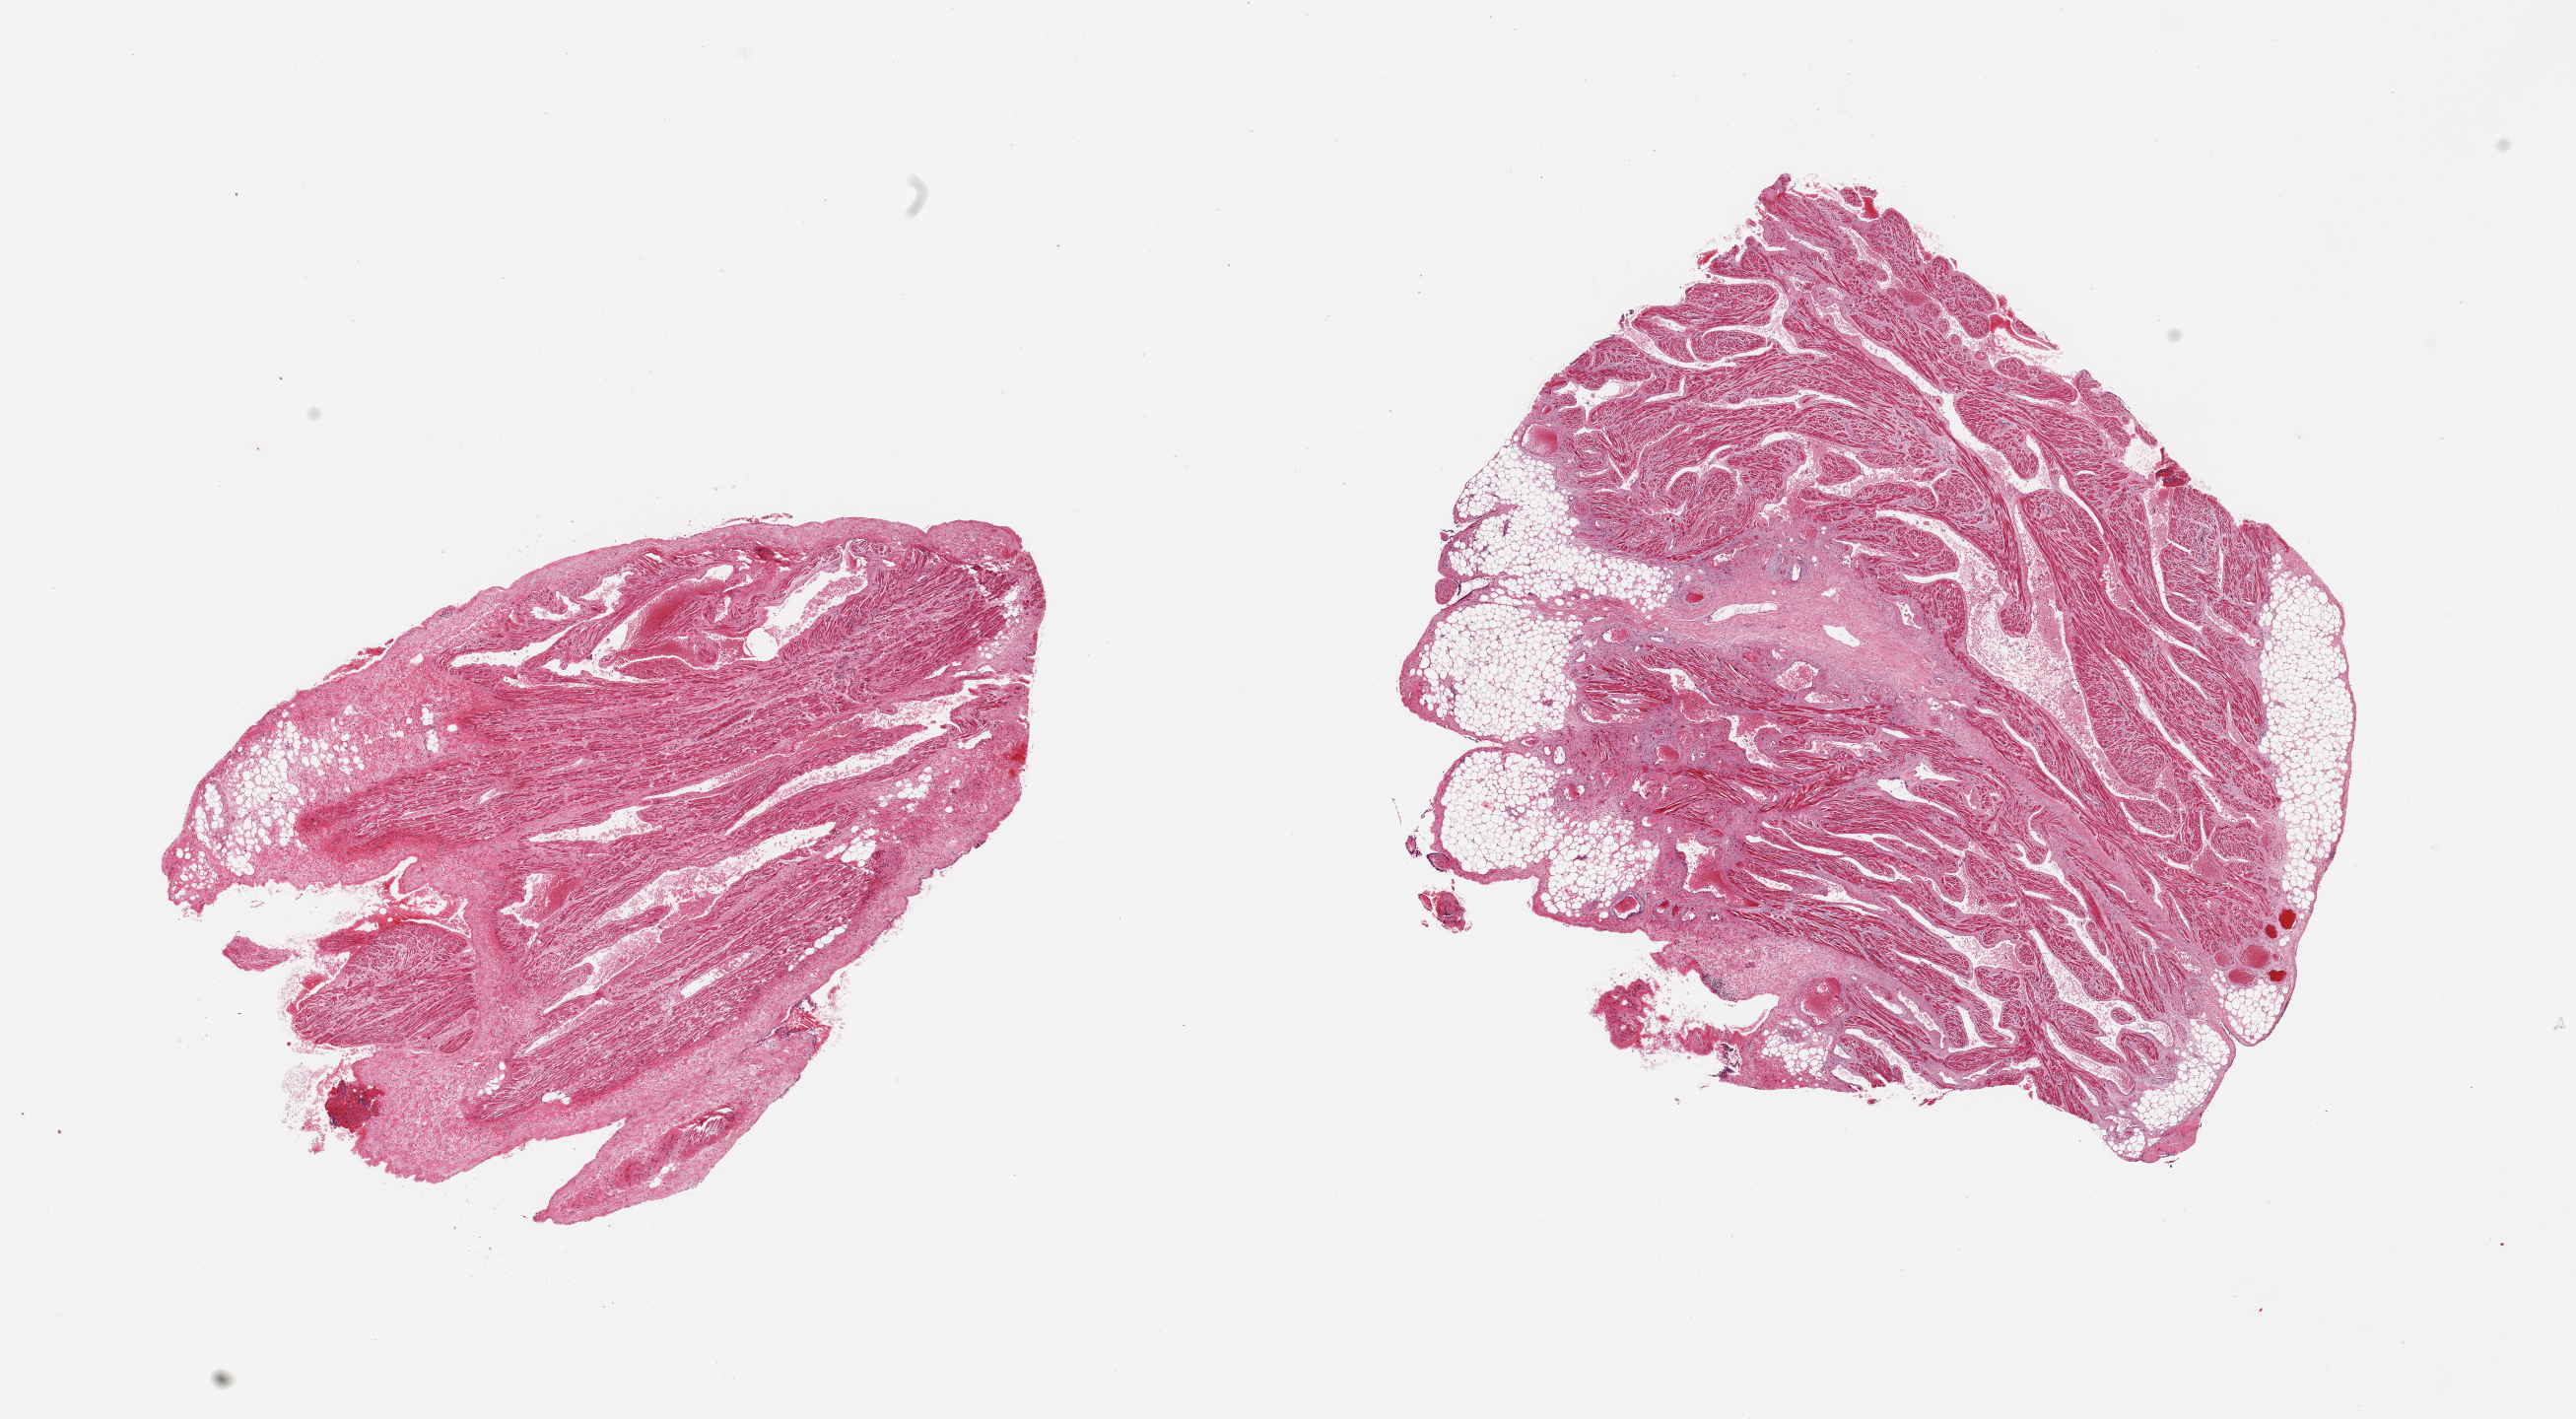
Whole-slide image, hematoxylin and eosin (H&E) stain — shown as a low-resolution overview of the whole scanned area (about 20.7 x 11.4 mm, from a 20x scan), PAXgene-fixed paraffin-embedded (PFPE) section, section of auricular appendage (target tissue), tissue donor sample. Female donor.
Review note (as recorded): 2 pieces; ~10% fat.